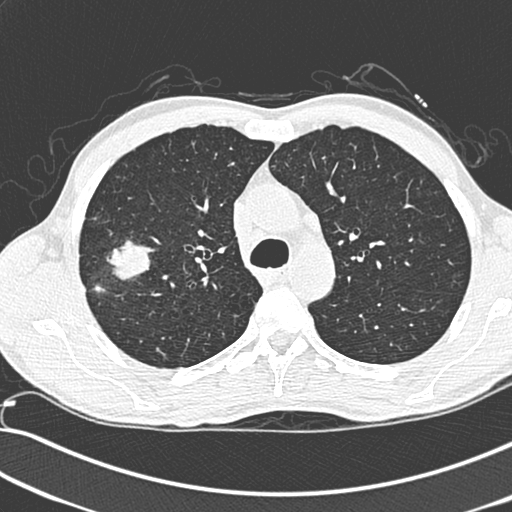
Low-dose screening chest CT, one axial slice. Position 210 of 281 along the scan axis. Lung window (W 1500 / L -600 HU). 1.3 mm slice thickness. 512 × 512 image matrix, field of view 341 × 341 mm.
Annotated regions visible in this slice (manually delineated by an expert):
- lesion 1 (tumor, upper lobe of right lung): box from (x=93, y=240) to (x=154, y=296) px